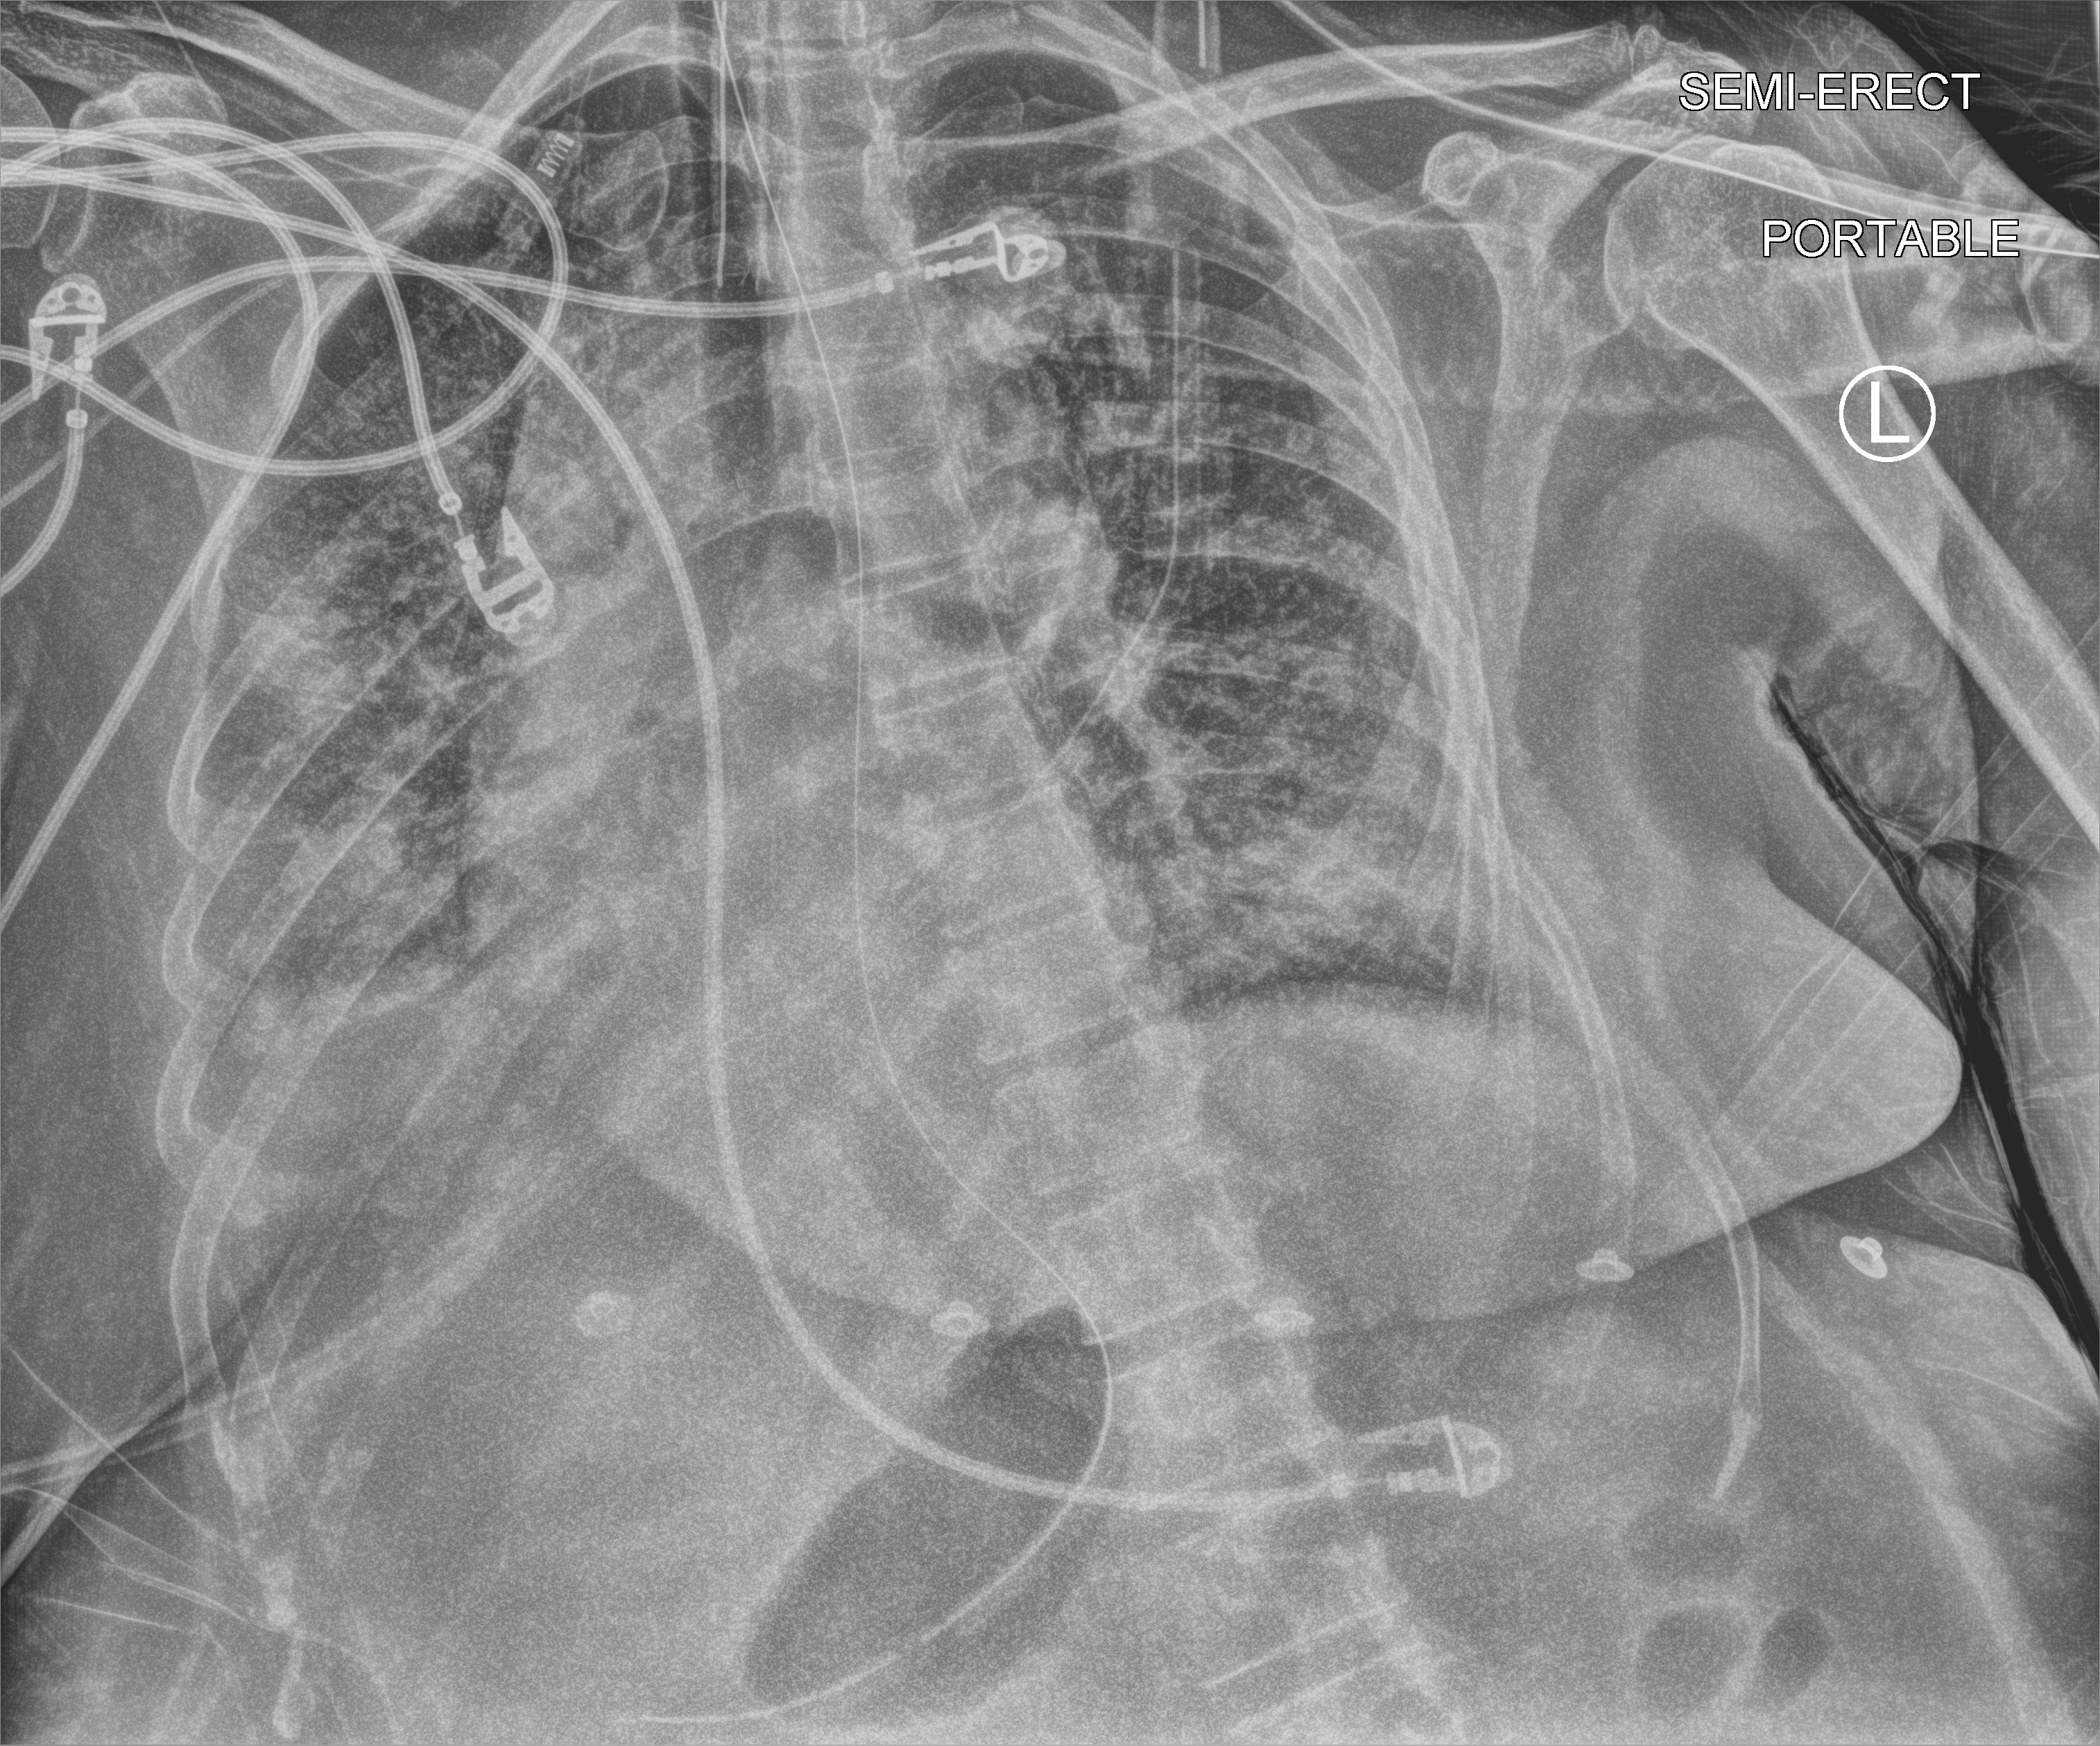
Portable chest radiograph, anteroposterior (AP) projection. Female patient hospitalised with COVID-19, age 18–59 years.
From the hospital-stay record, not from the radiograph (when in the stay this image was taken is not recorded):
- admitted to intensive care during this hospital stay: yes
- smoking status (admission record): never
- chronic kidney disease (admission record): no